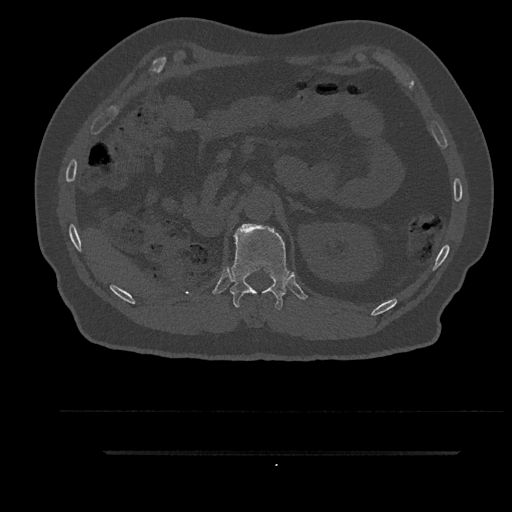
CT including the spine, one axial slice. Position 244 of 797 along the scan axis. Reconstruction kernel Br40s/3. Bone window (W 1800 / L 400 HU). 512 × 512 image matrix, field of view 432 × 432 mm. Male patient, age 63 years. From the clinical record (not read from this slice): primary cancer: renal.
Annotated regions visible in this slice (semi-automatically segmented with operator editing):
- T12 vertebra: bounding box (x1, y1, x2, y2) in pixels: (229, 224, 290, 310)